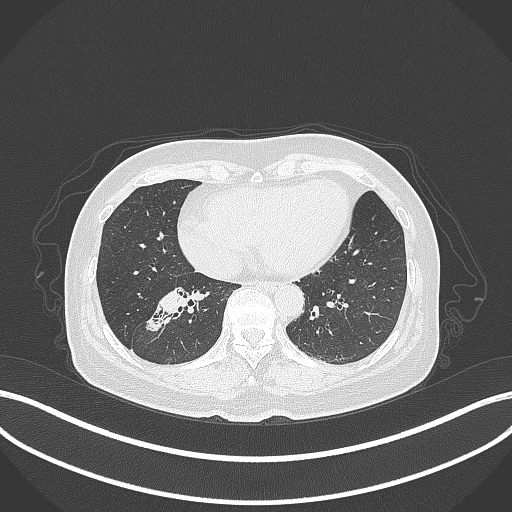
Chest CT, one axial slice; slice 137 of 429 in the series (ordered by position); reconstruction kernel B70f; 120 kVp; lung window (W 1500 / L -600 HU); 1 mm slice thickness; 512 × 512 image matrix, field of view 400 × 400 mm. Patient: female, 67 years. Case-level facts recorded for this patient, not image findings: clinical TNM (as recorded): T1c N1 M0; histopathological grade: G2-3.
Annotated regions visible in this slice (bounding box drawn by a radiologist):
- lung tumour (recorded histology: adenocarcinoma): bounding box <140,284,193,335> (left, top, right, bottom; pixels)